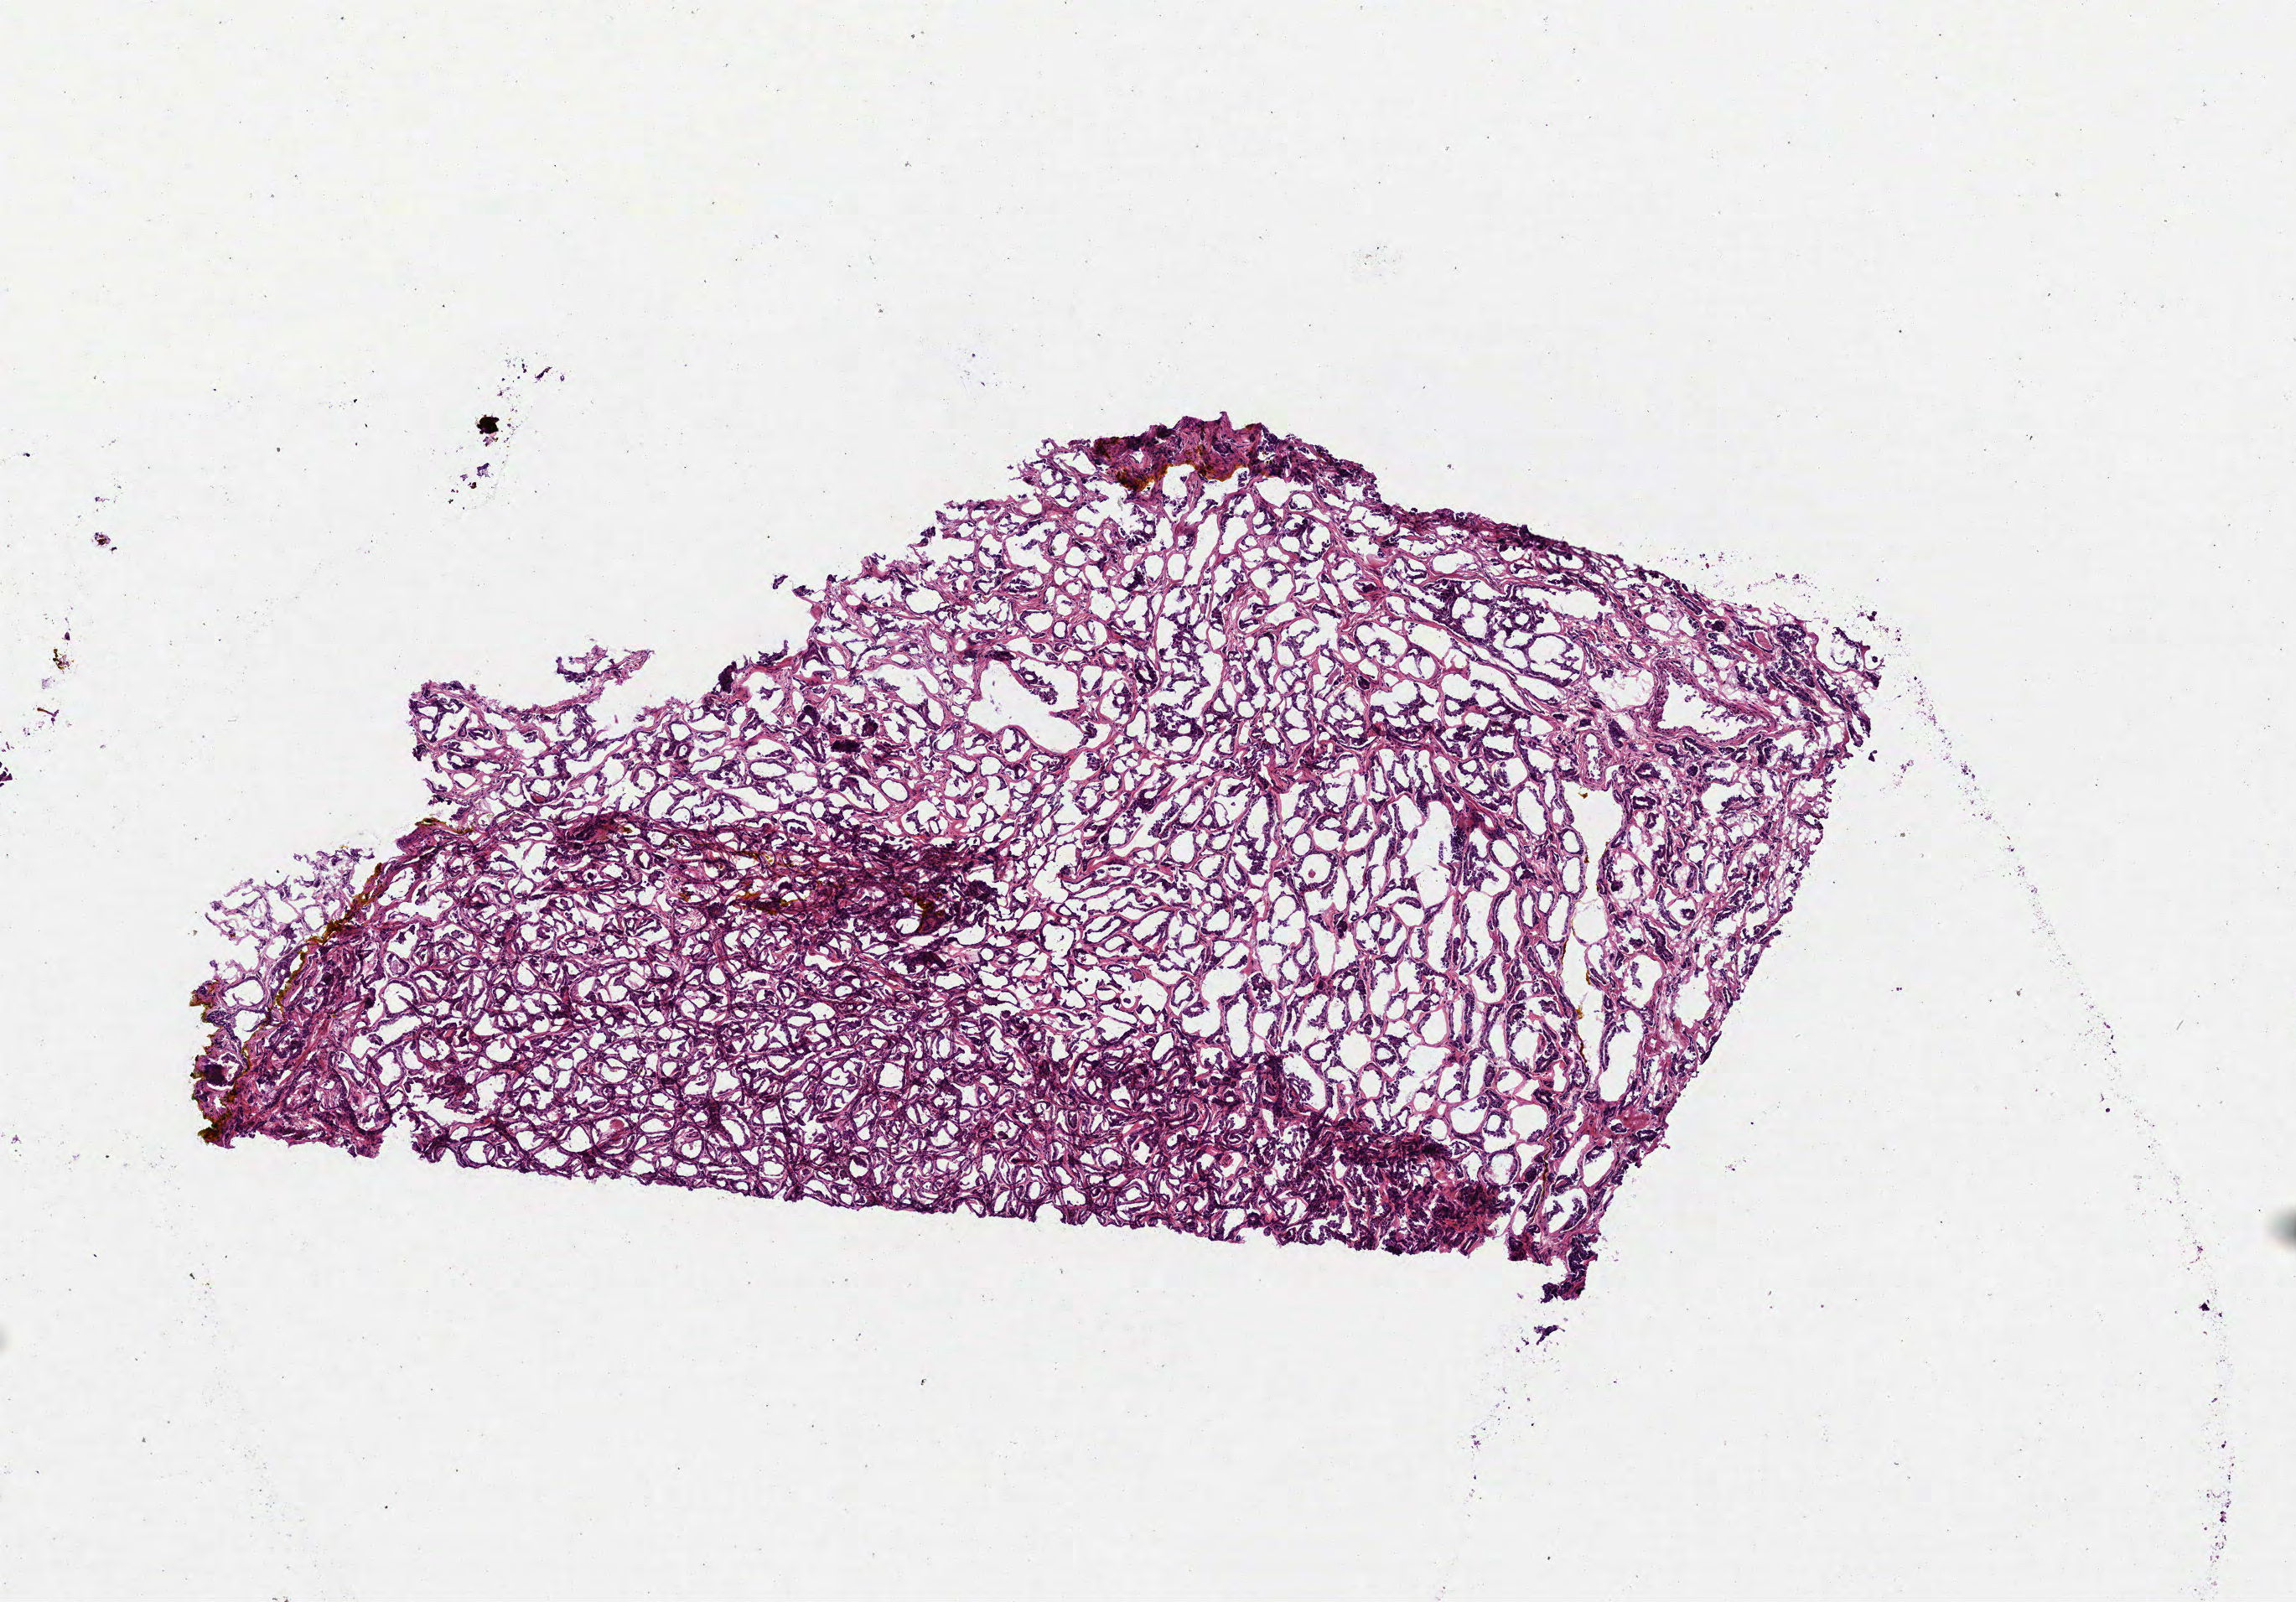
Whole-slide histology image, H&E — shown as a low-resolution overview of the whole scanned area (about 5.5 x 3.9 mm, slide scanned at 40x); frozen section; sample: primary tumour, prostate. Male, age 61 years at initial diagnosis. Gleason score: 7 (3+4). Slide review estimates, as recorded: tumour cells 80%, tumour nuclei 80%, normal cells 5%, stromal cells 15%, necrosis 0%. Inflammatory infiltration, as recorded: lymphocyte infiltration 0%, monocyte infiltration 0%, neutrophil infiltration 0%.
* laterality: bilateral
* pathologic diagnosis: Acinar cell carcinoma (prostate gland)
* lymph nodes positive (case pathology): 0 of 6 examined